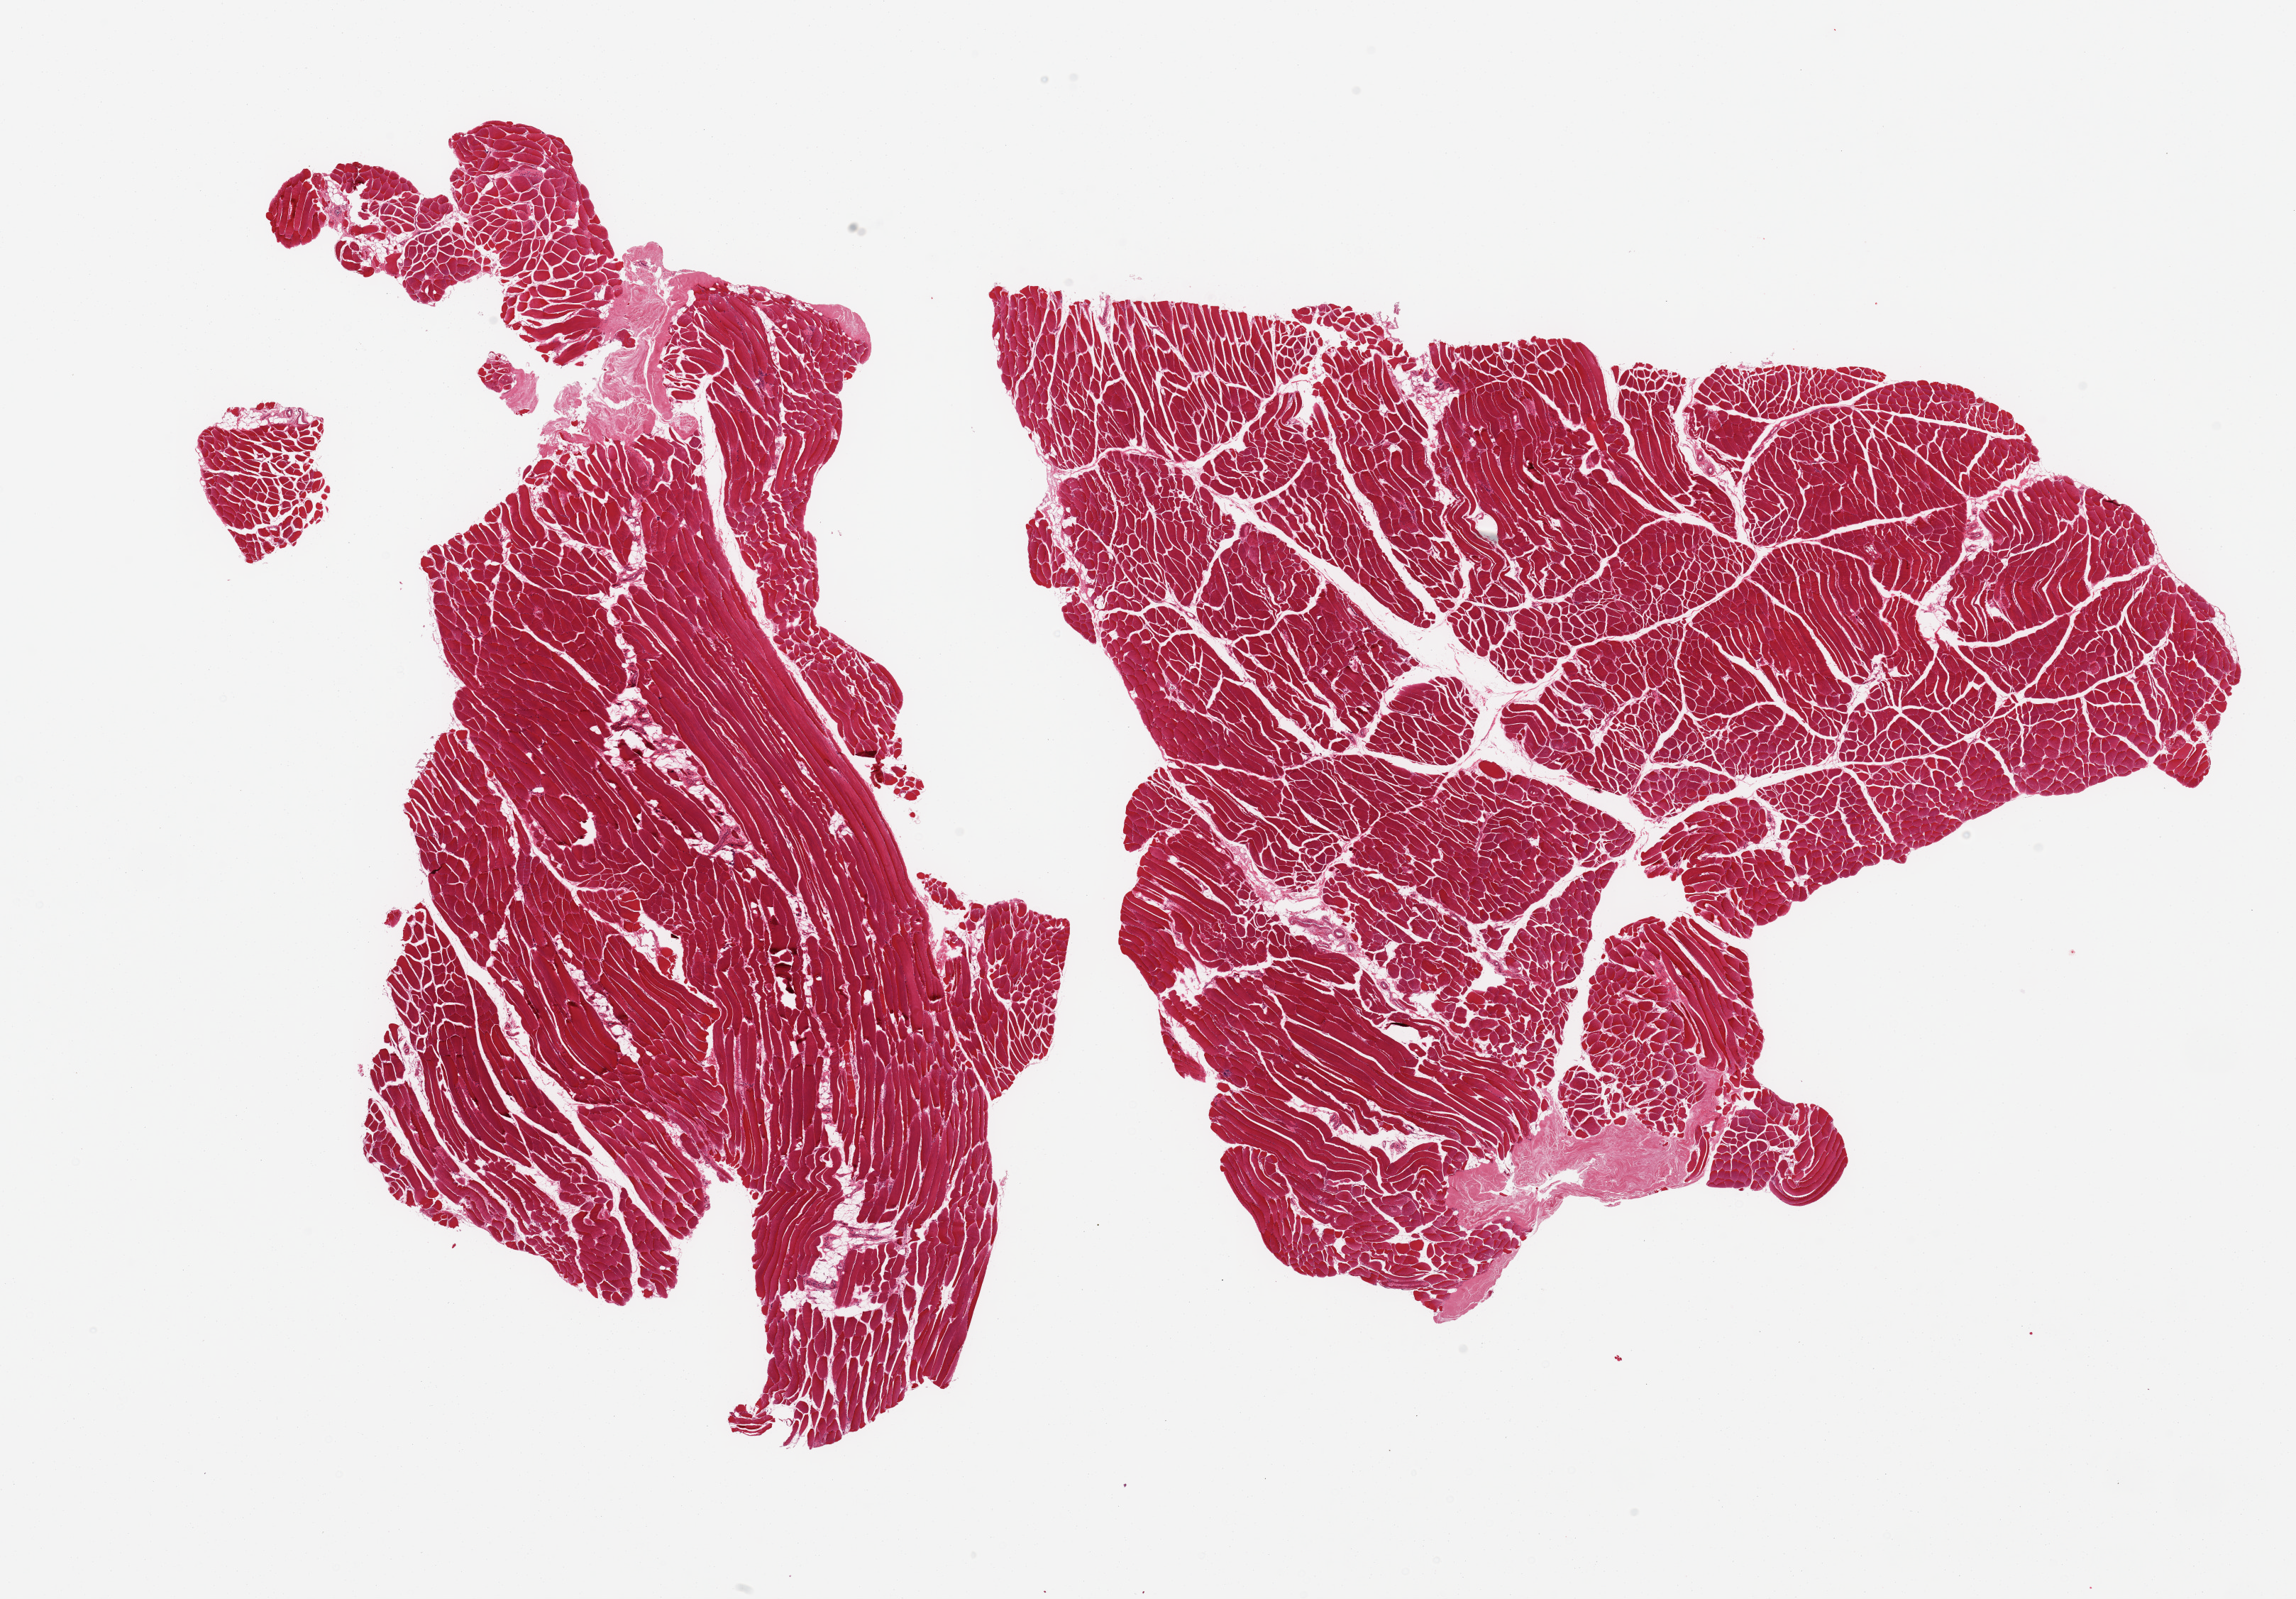
Whole-slide image, H&E stain, brightfield — low-resolution overview of the scanned area, about 25.6 x 17.8 mm, PAXgene-fixed paraffin-embedded (PFPE) section, section of skeletal muscle (target tissue), tissue donor sample.
* pathologist's review note for this sample: 2 pieces; foci of tendon in each piece up to 2.5 mm at edge